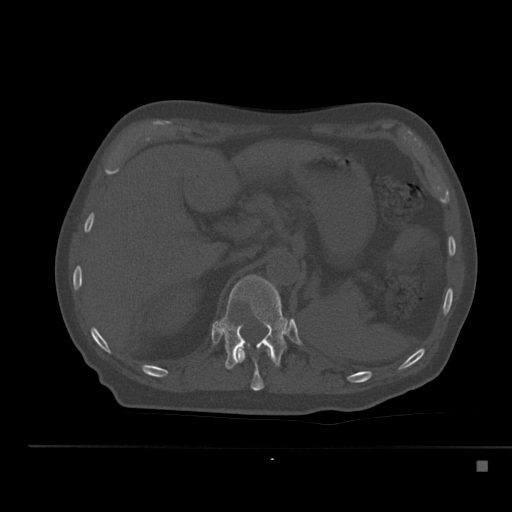
CT including the spine, one axial slice; slice 233 of 517 in the series (ordered by position); reconstruction kernel Br40s; 120 kVp; bone window (W 1800 / L 400 HU); 1.5 mm slice thickness; 512 × 512 image matrix, field of view 408 × 408 mm. Patient: male, 70 years. From the clinical record (not read from this slice): primary cancer: renal; vertebrae with lytic lesions (as recorded): T4, T6, T10, T12, L3, L4, L5.
Structures marked on this image (semi-automatic segmentation, software-assisted and operator-edited):
- T11 vertebra: box from (x=236, y=347) to (x=273, y=391) px
- T12 vertebra: (x=216, y=275)–(x=290, y=370)